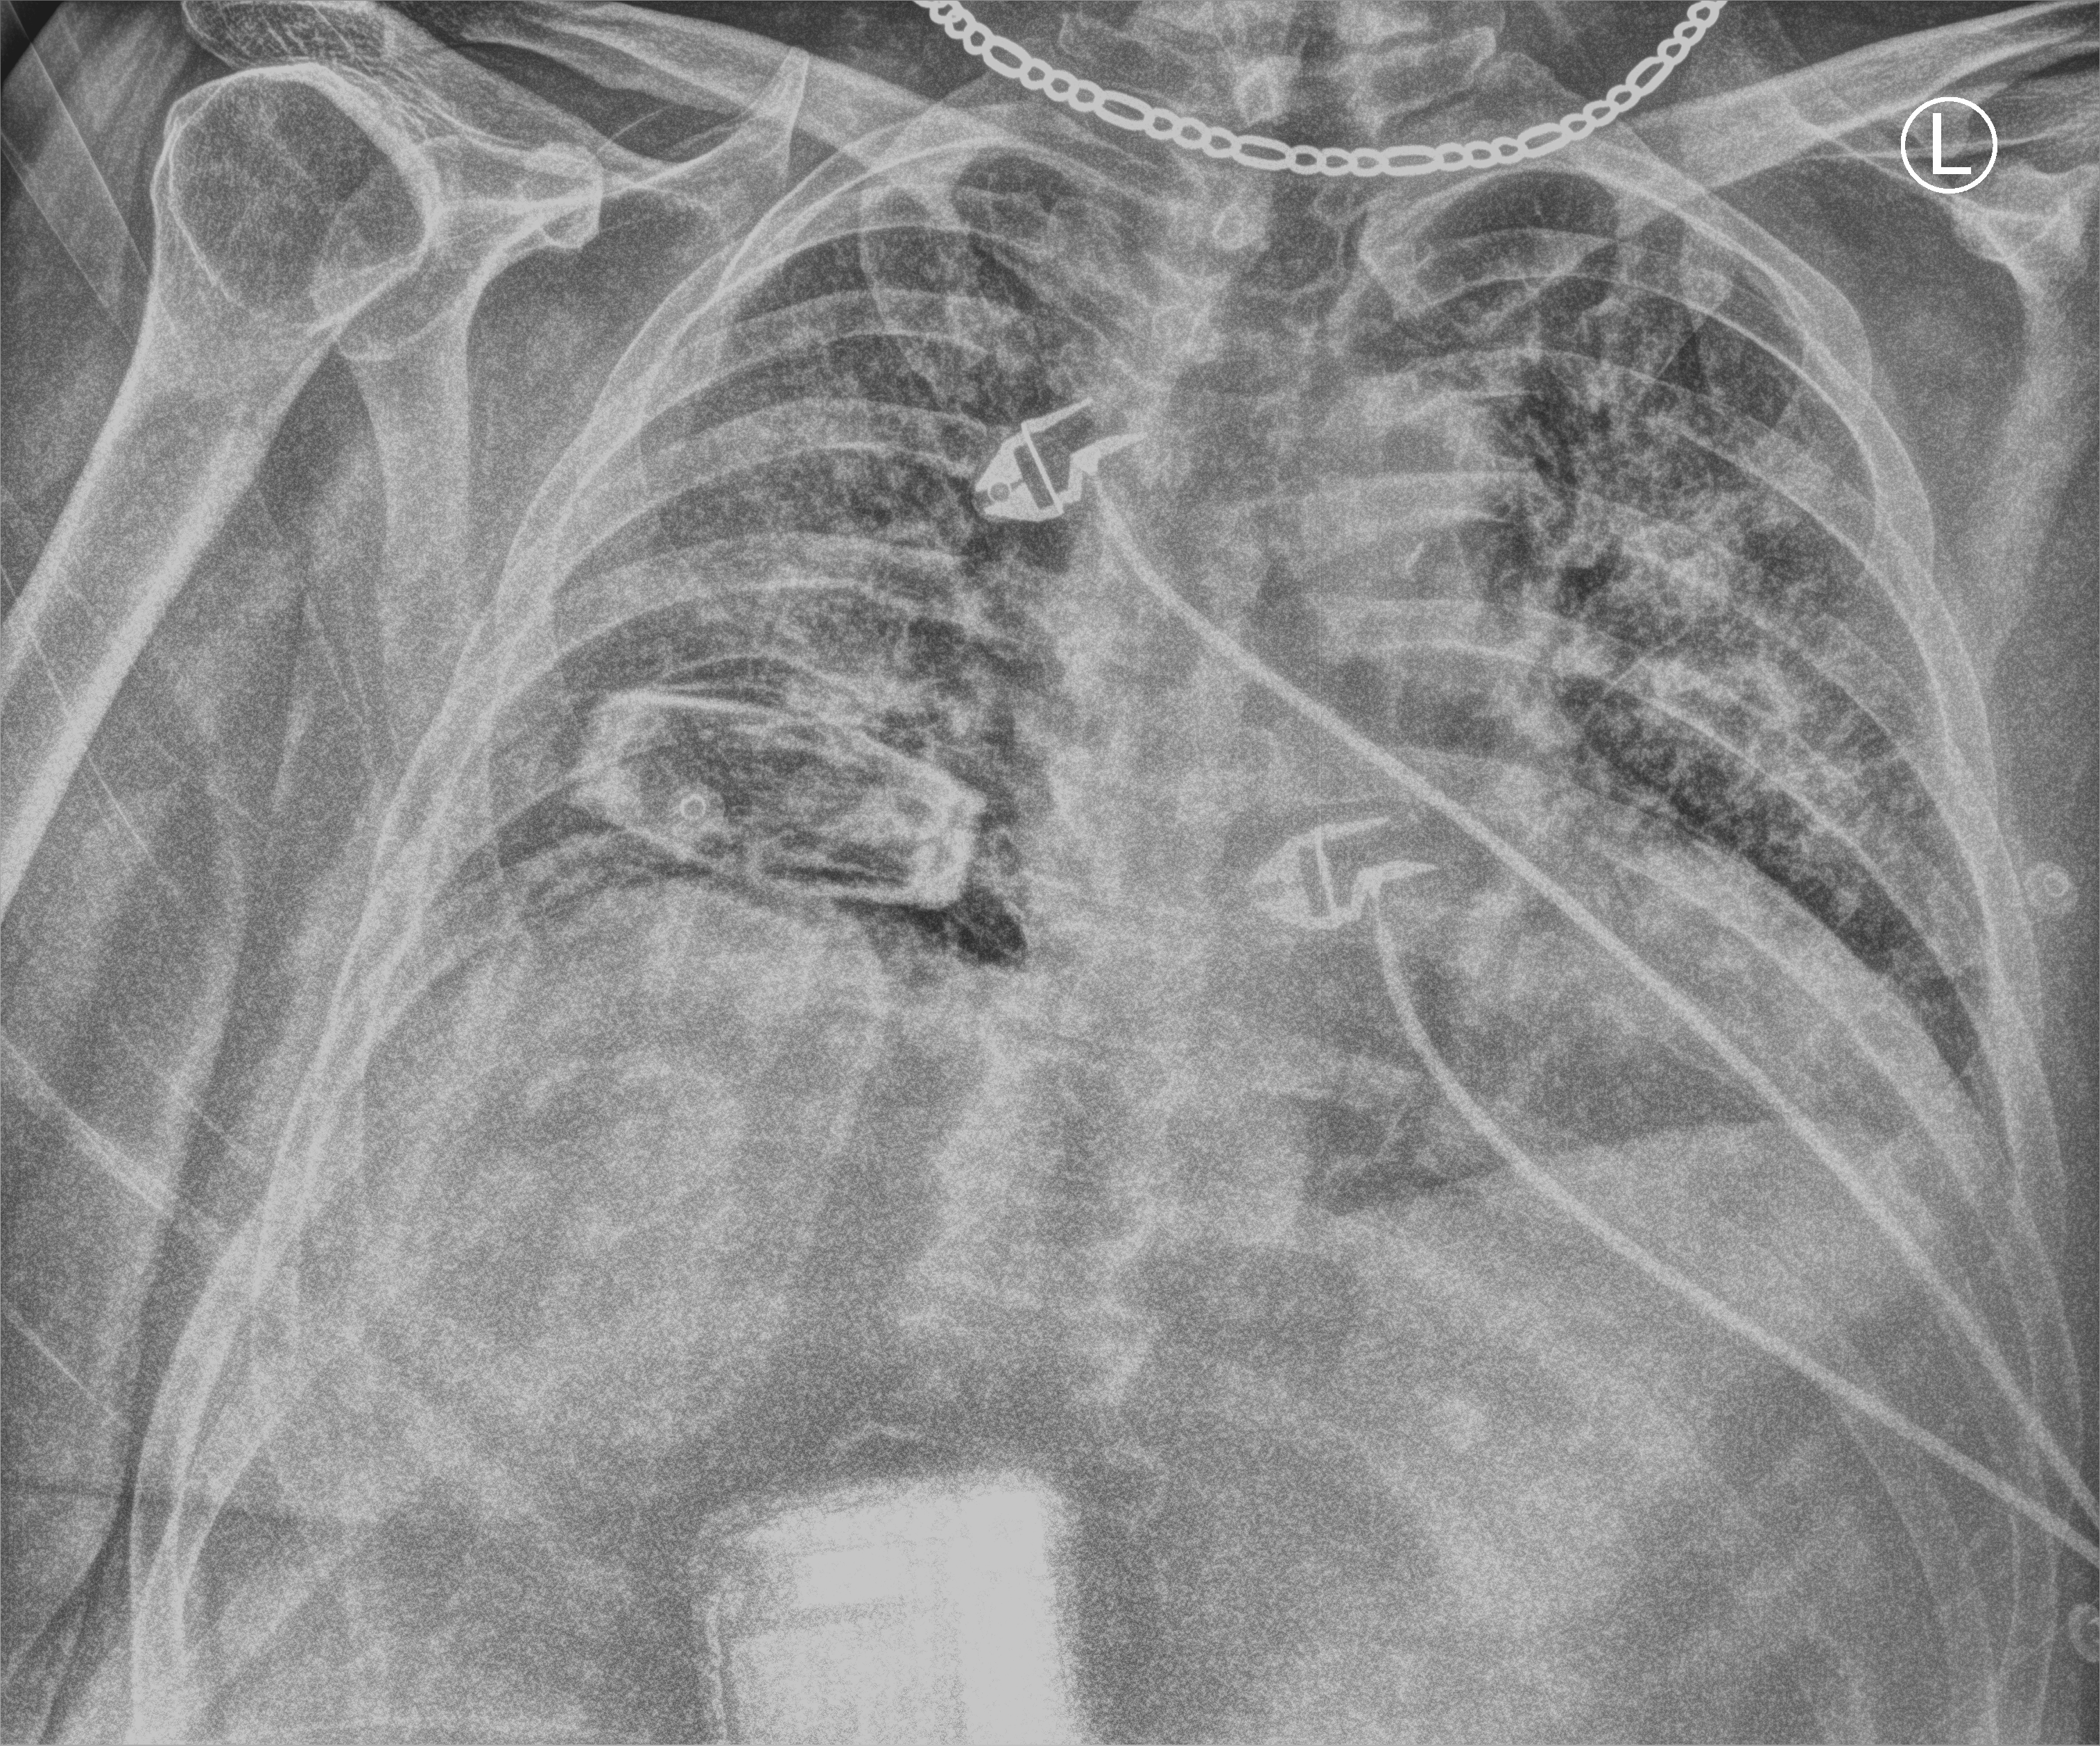
Portable chest radiograph, anteroposterior (AP) projection. Male patient hospitalised with COVID-19, age 60–74 years.
Hospital-stay facts (about this admission, not read from this image; timing relative to this image not recorded): admitted to intensive care during this hospital stay: no; mechanically ventilated during this hospital stay: no.